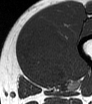
MRI of an extremity soft-tissue mass, one axial slice; position 19 of 62 along the scan axis; MR volume resampled by the dataset authors to the PET/CT grid (not the native acquisition matrix); 3.27 mm slice thickness; 92 × 104 image matrix, field of view 90 × 102 mm. Male patient. Case-level facts recorded for this patient, not image findings: histological type: mixoid liposarcoma; grade: low; site of the primary tumour: left thigh.
Annotated regions visible in this slice (expert contour drawn on MRI and transferred to this co-registered scan by the dataset authors):
- gross tumour volume (mass): box from (x=23, y=23) to (x=68, y=84) px